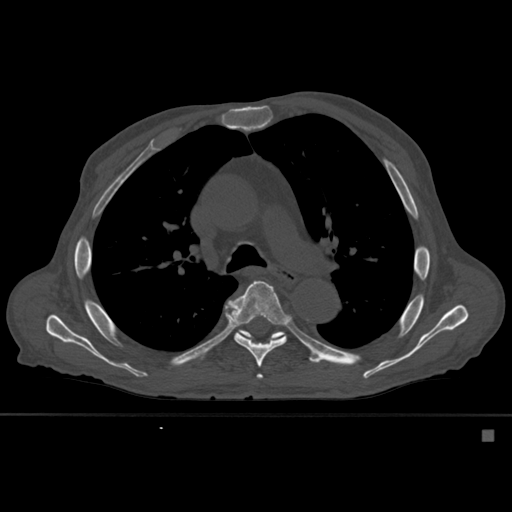
CT including the spine, one axial slice; slice 382 of 527 in the series (ordered by position); bone window (W 1800 / L 400 HU); 1.5 mm slice thickness; 512 × 512 image matrix, field of view 373 × 373 mm. Male patient, age 78 years. From the clinical record (not read from this slice): primary cancer: prostate.
Annotated regions visible in this slice (semi-automatic segmentation, software-assisted and operator-edited):
- T5 vertebra: bounding box <257,374,263,379> (left, top, right, bottom; pixels)
- T6 vertebra: <225,280,291,368>
- T7 vertebra: <238,329,285,341>